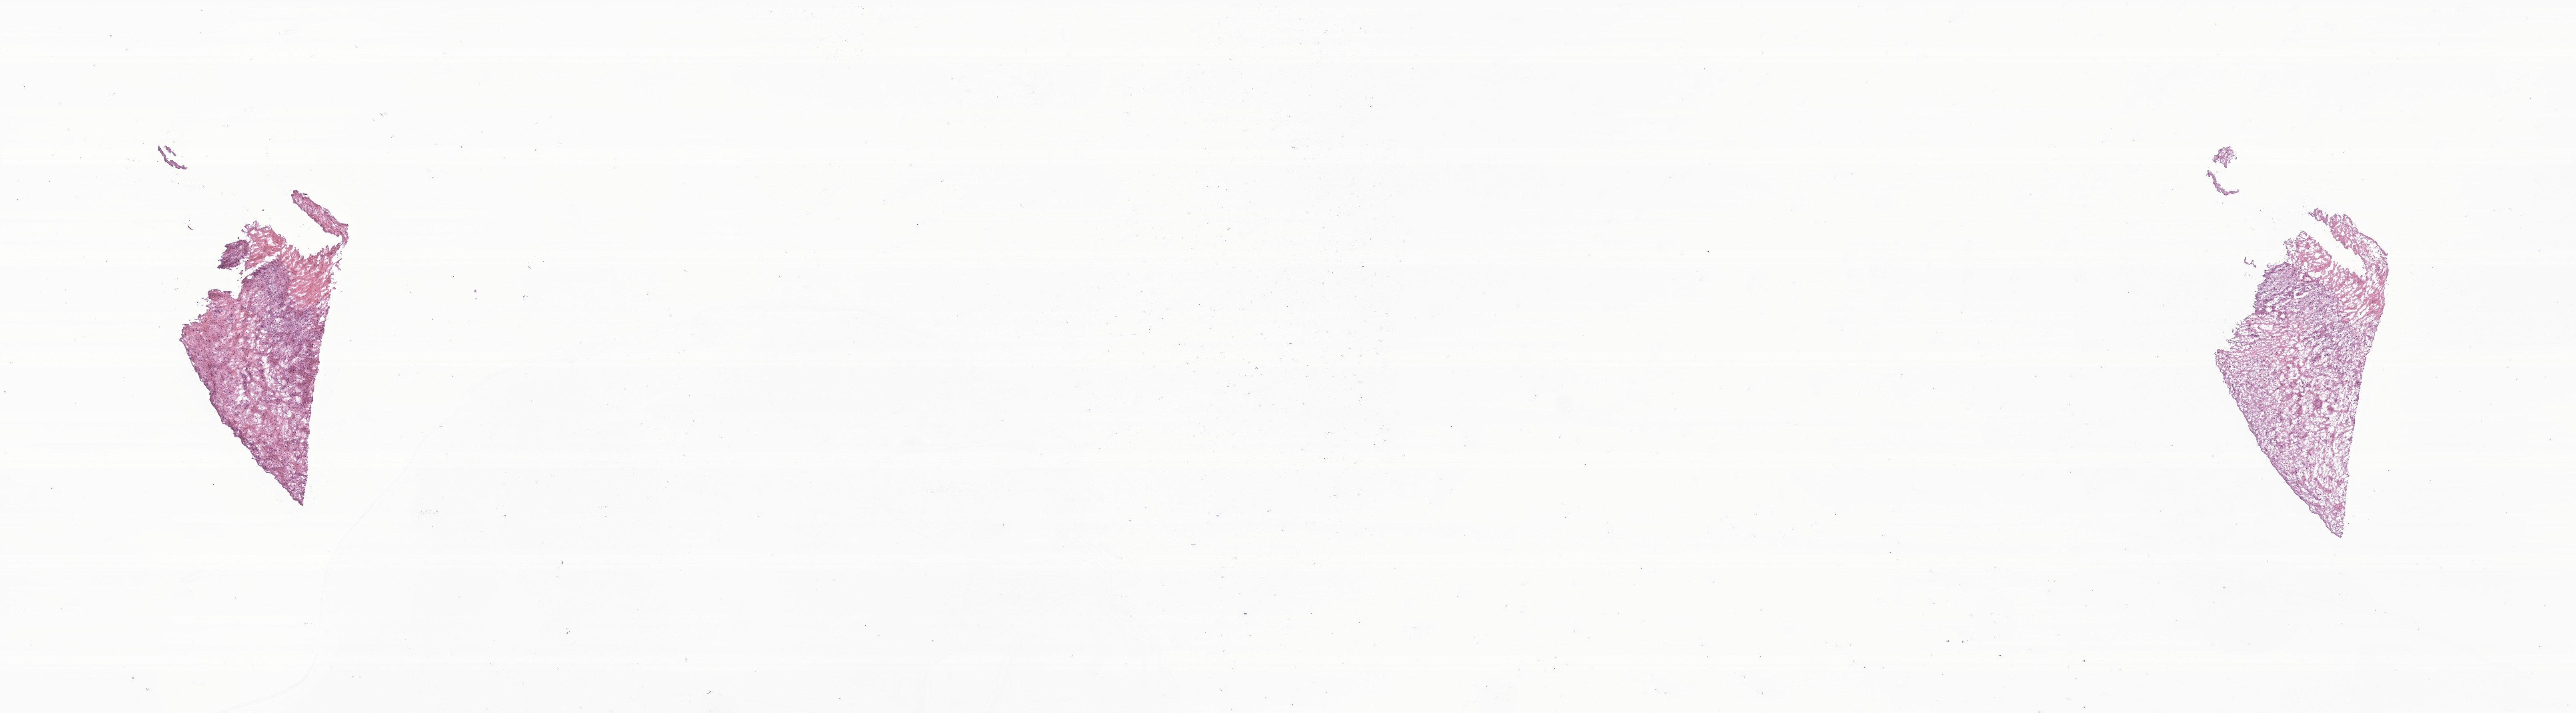
Haematoxylin and eosin whole-slide image of tumor tissue from the soft tissue of thorax — a low-resolution overview of the entire scanned area, about 27.2 x 7.5 mm; frozen section. Patient female; age 241 days.
Recorded diagnosis: Spindle cell rhabdomyosarcoma.